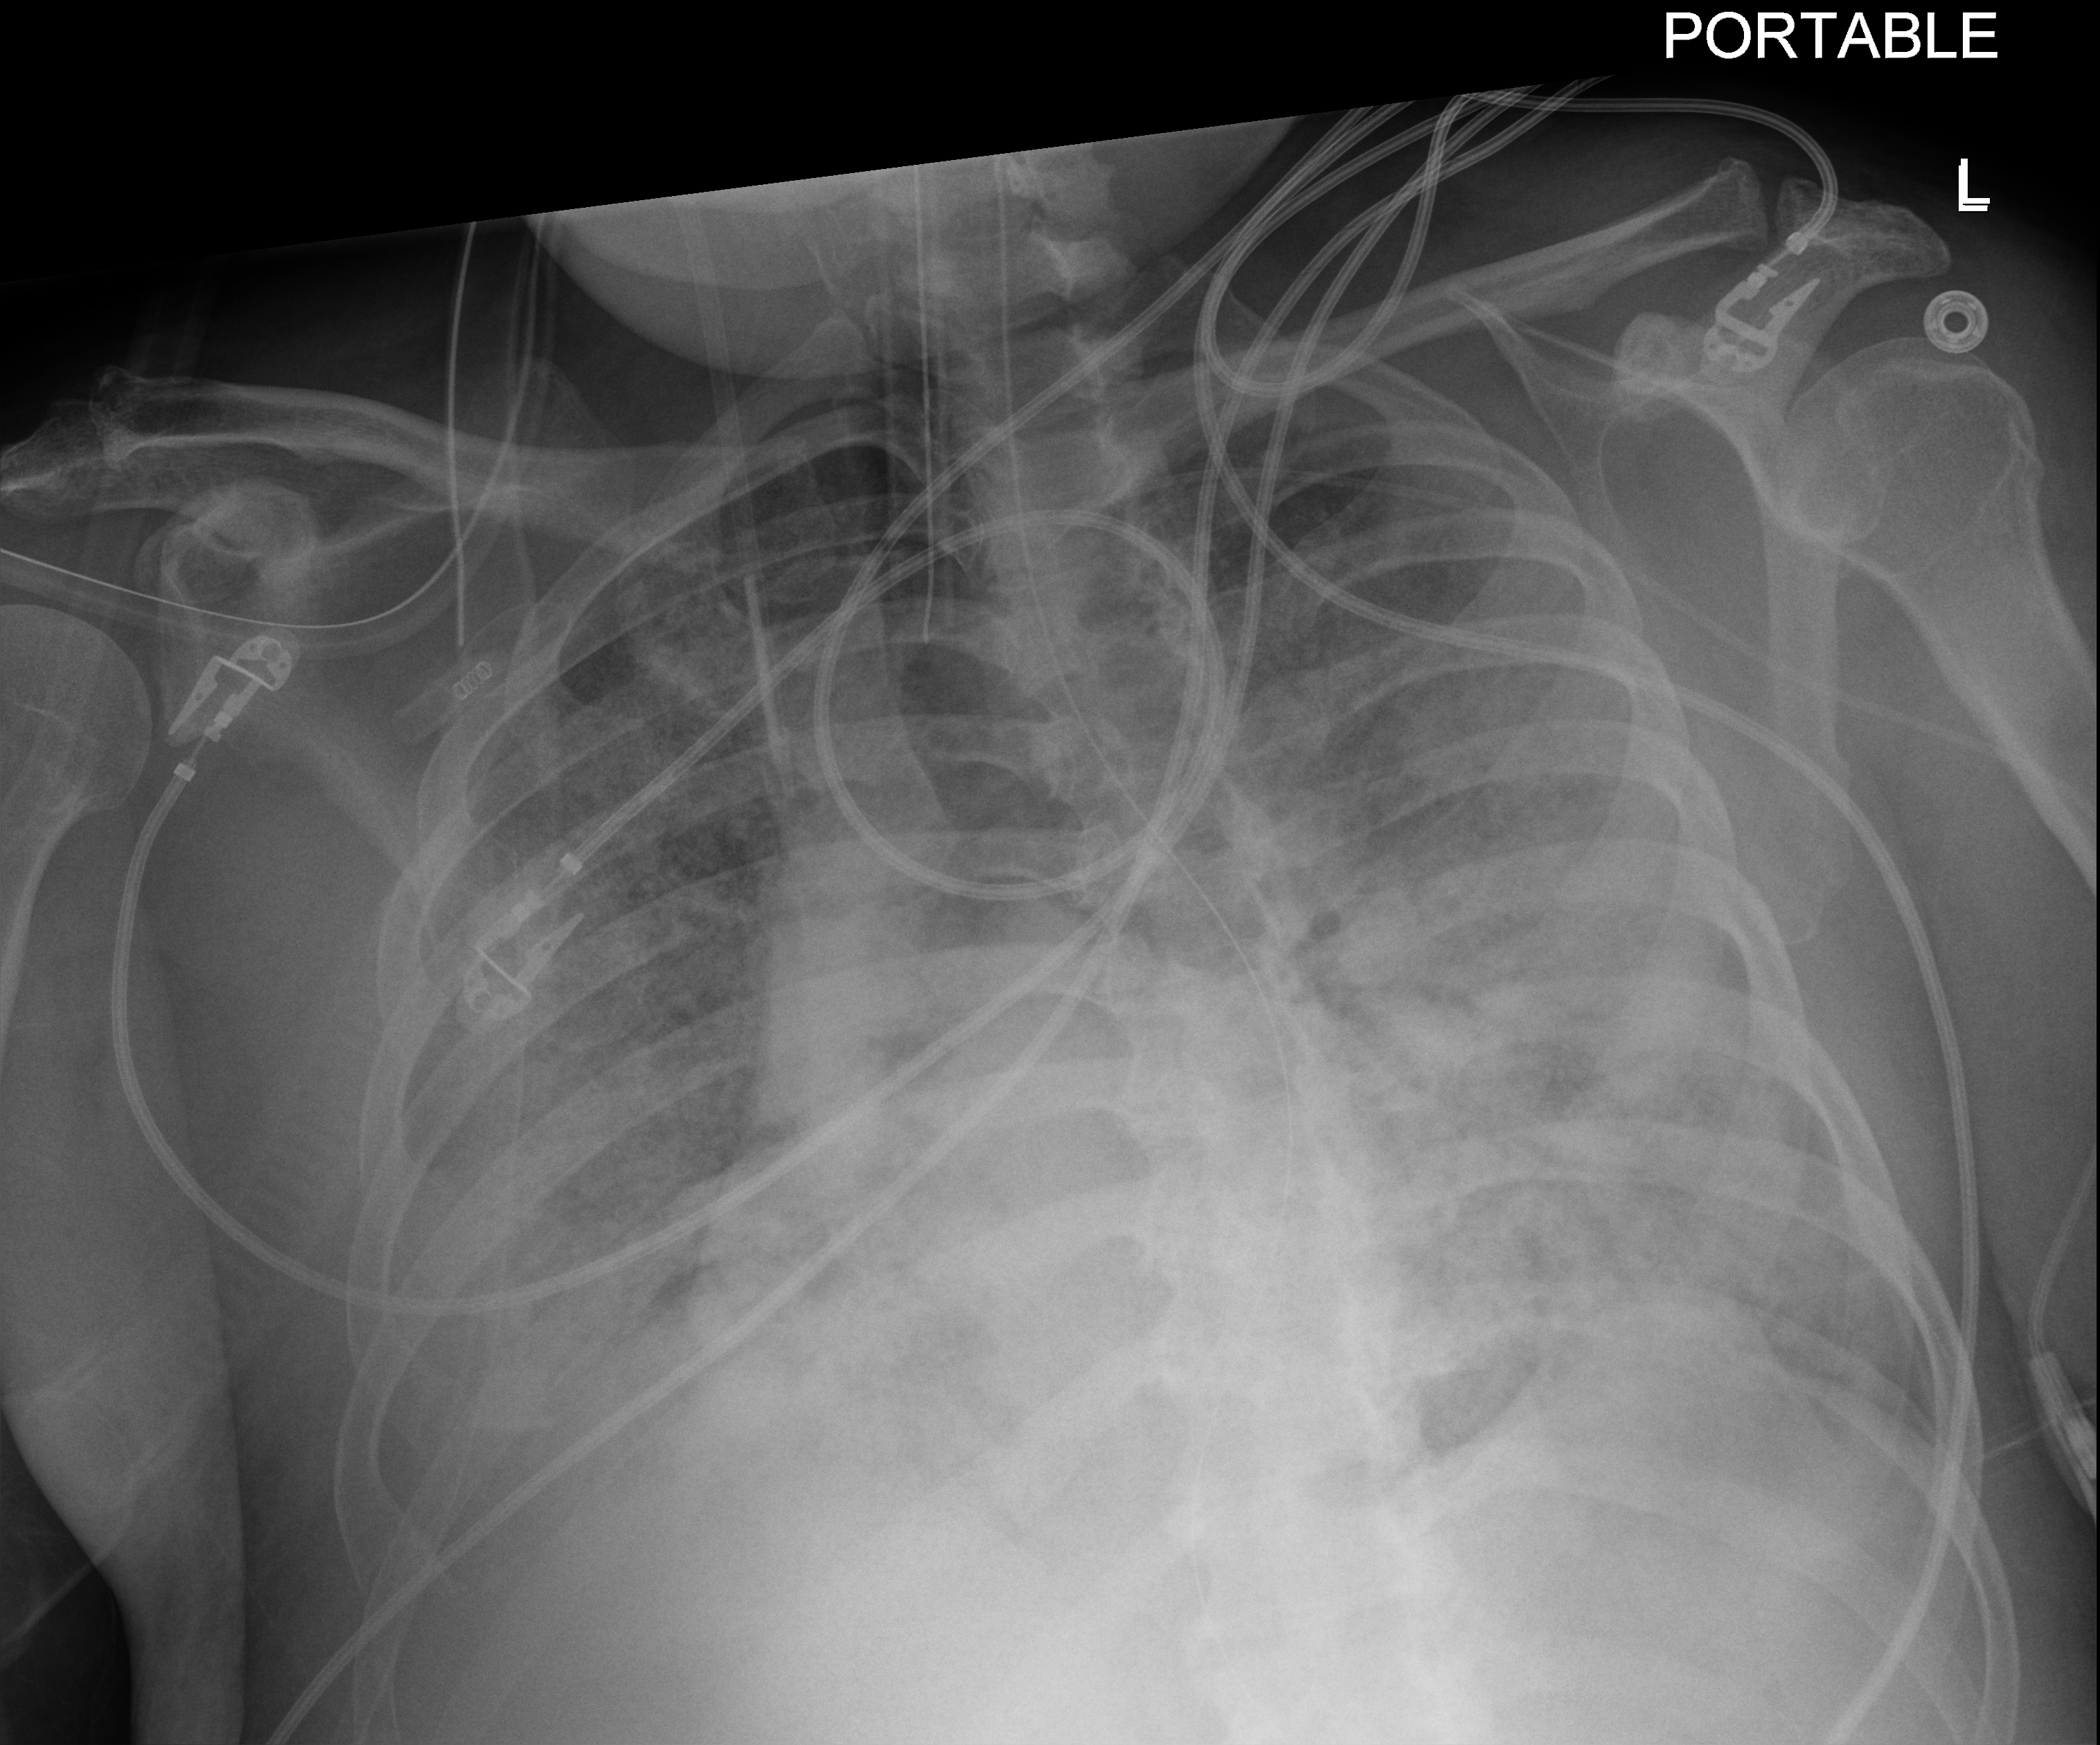
Bedside chest radiograph (digital radiography). Male patient hospitalised with COVID-19, age 60–74 years.
Admission-level facts for this patient (not findings on this image; timing relative to this image not recorded): length of hospital stay: 28 days; mechanically ventilated during this hospital stay: yes; smoking status (admission record): never.